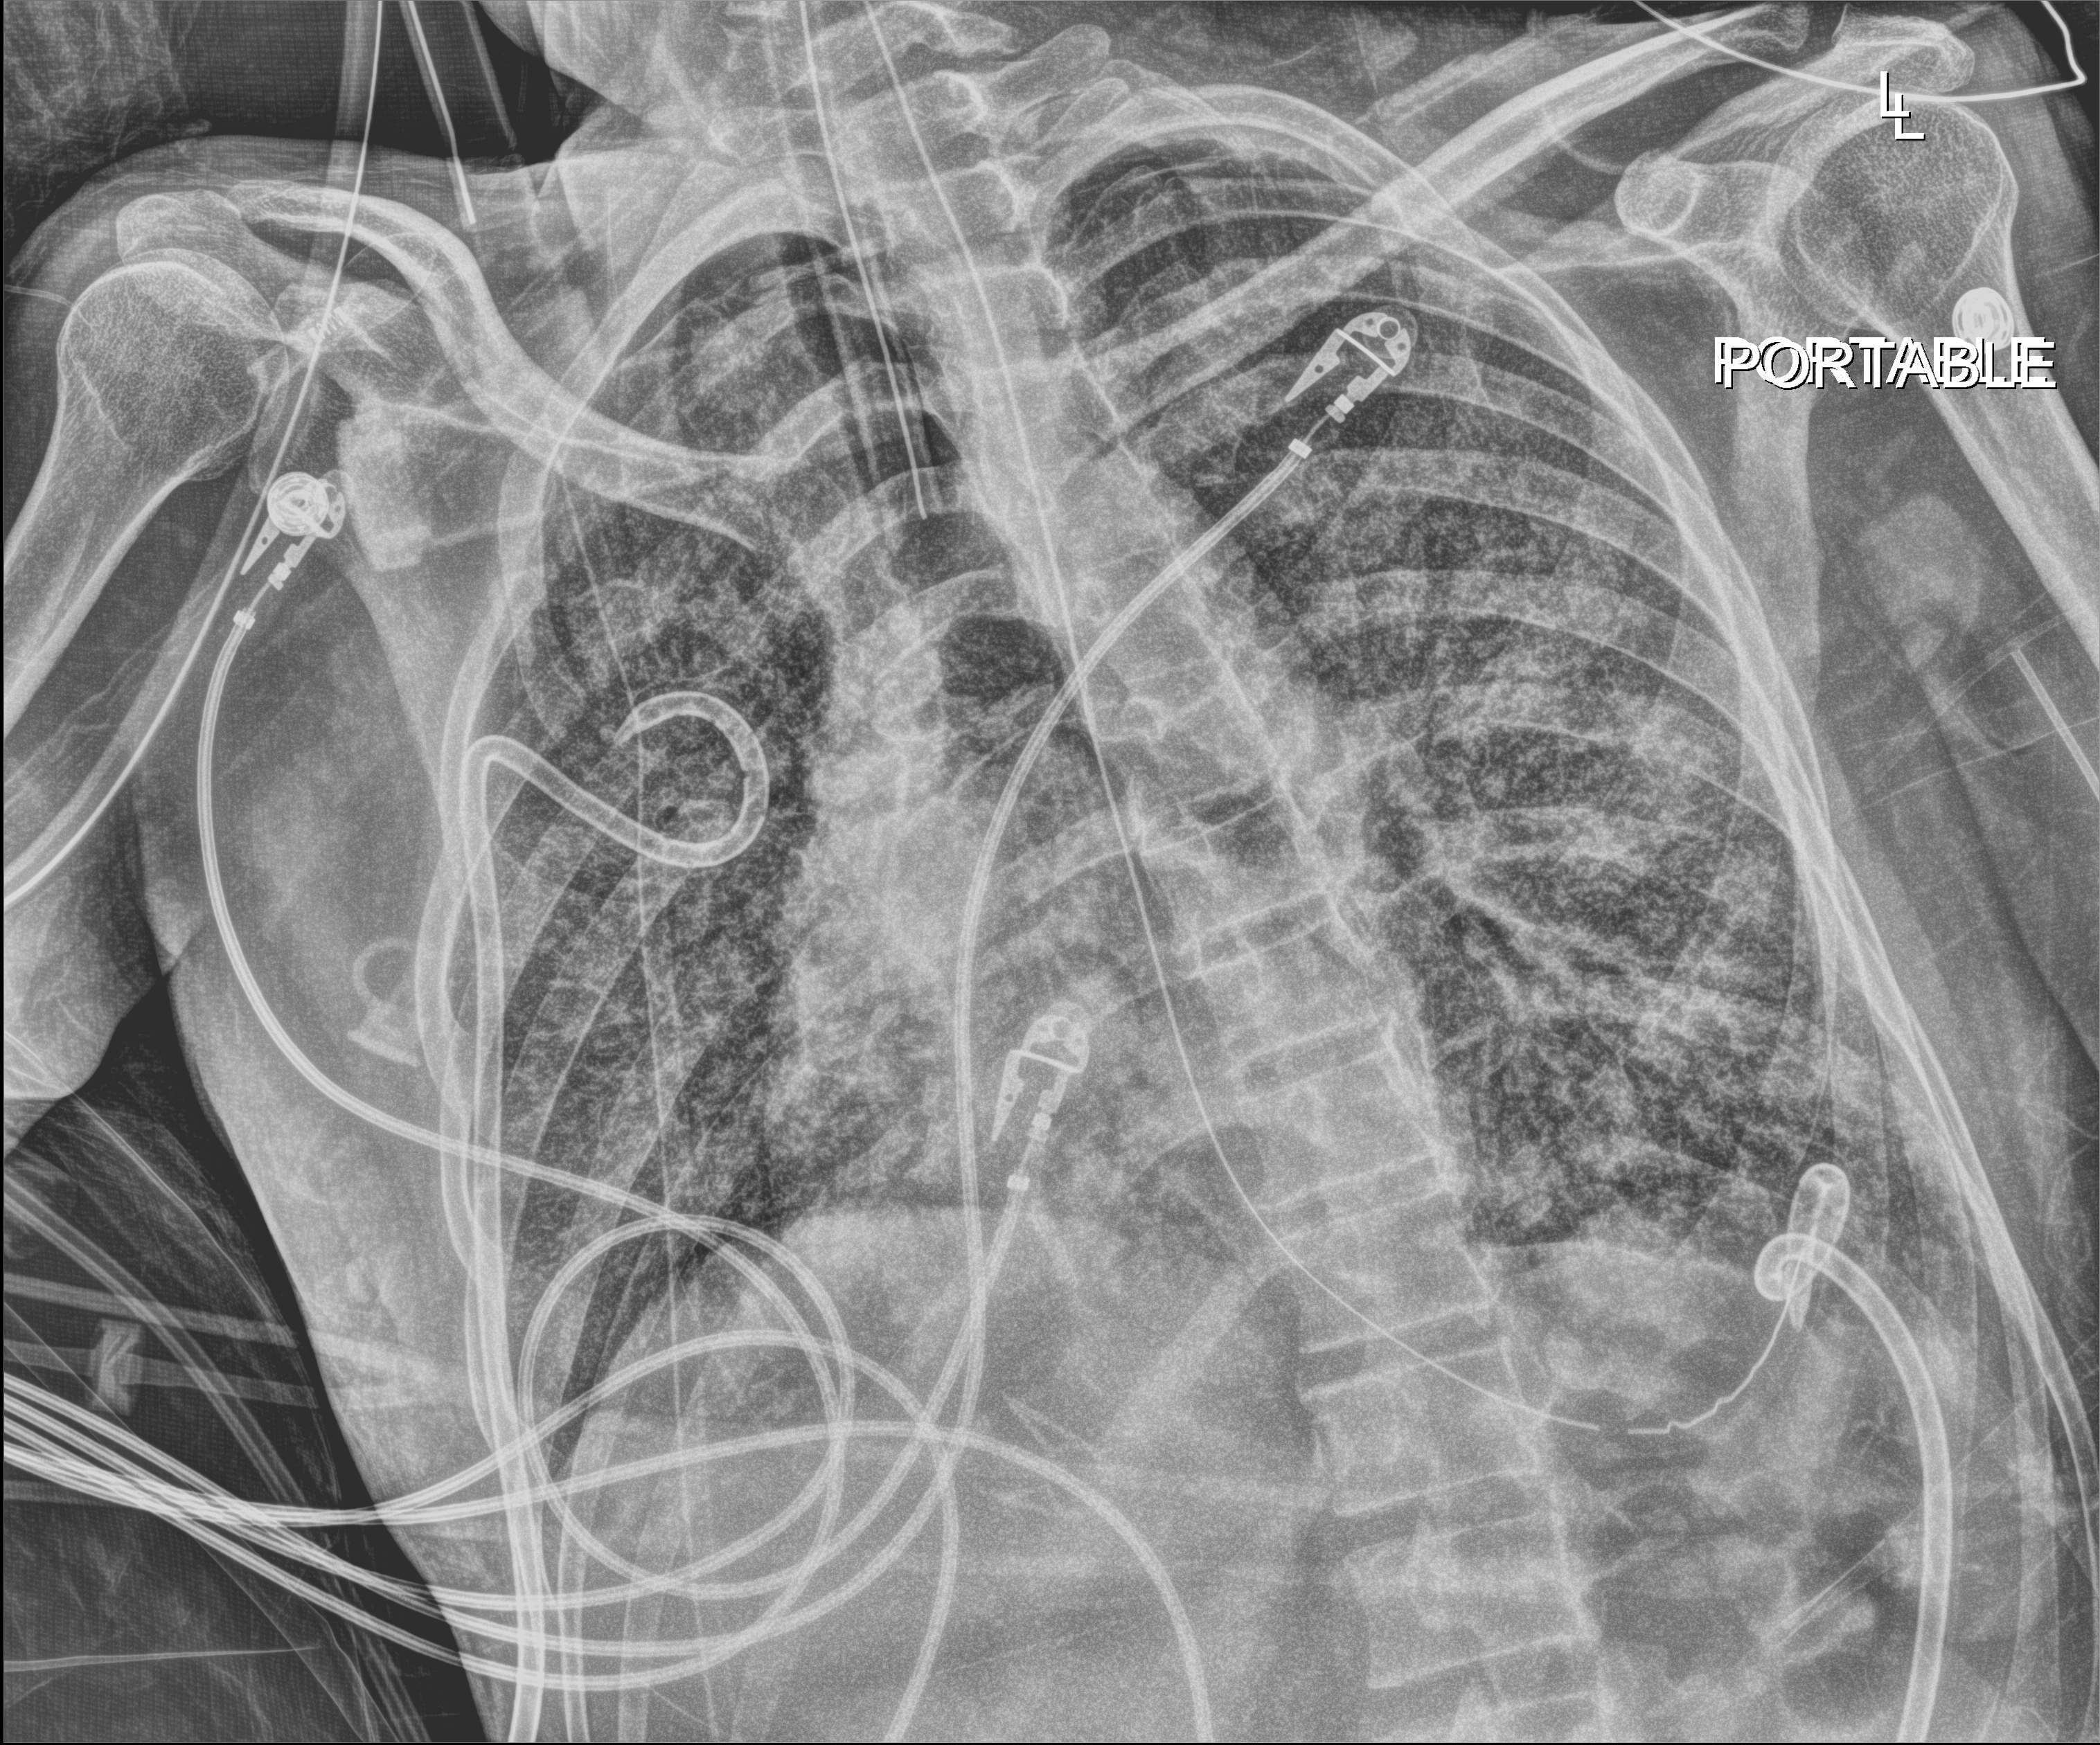
Bedside chest radiograph (digital radiography), anteroposterior (AP) projection. Patient hospitalised with COVID-19, aged 18–59 years.
From the hospital-stay record, not from the radiograph (when in the stay this image was taken is not recorded): admitted to intensive care during this hospital stay: yes.